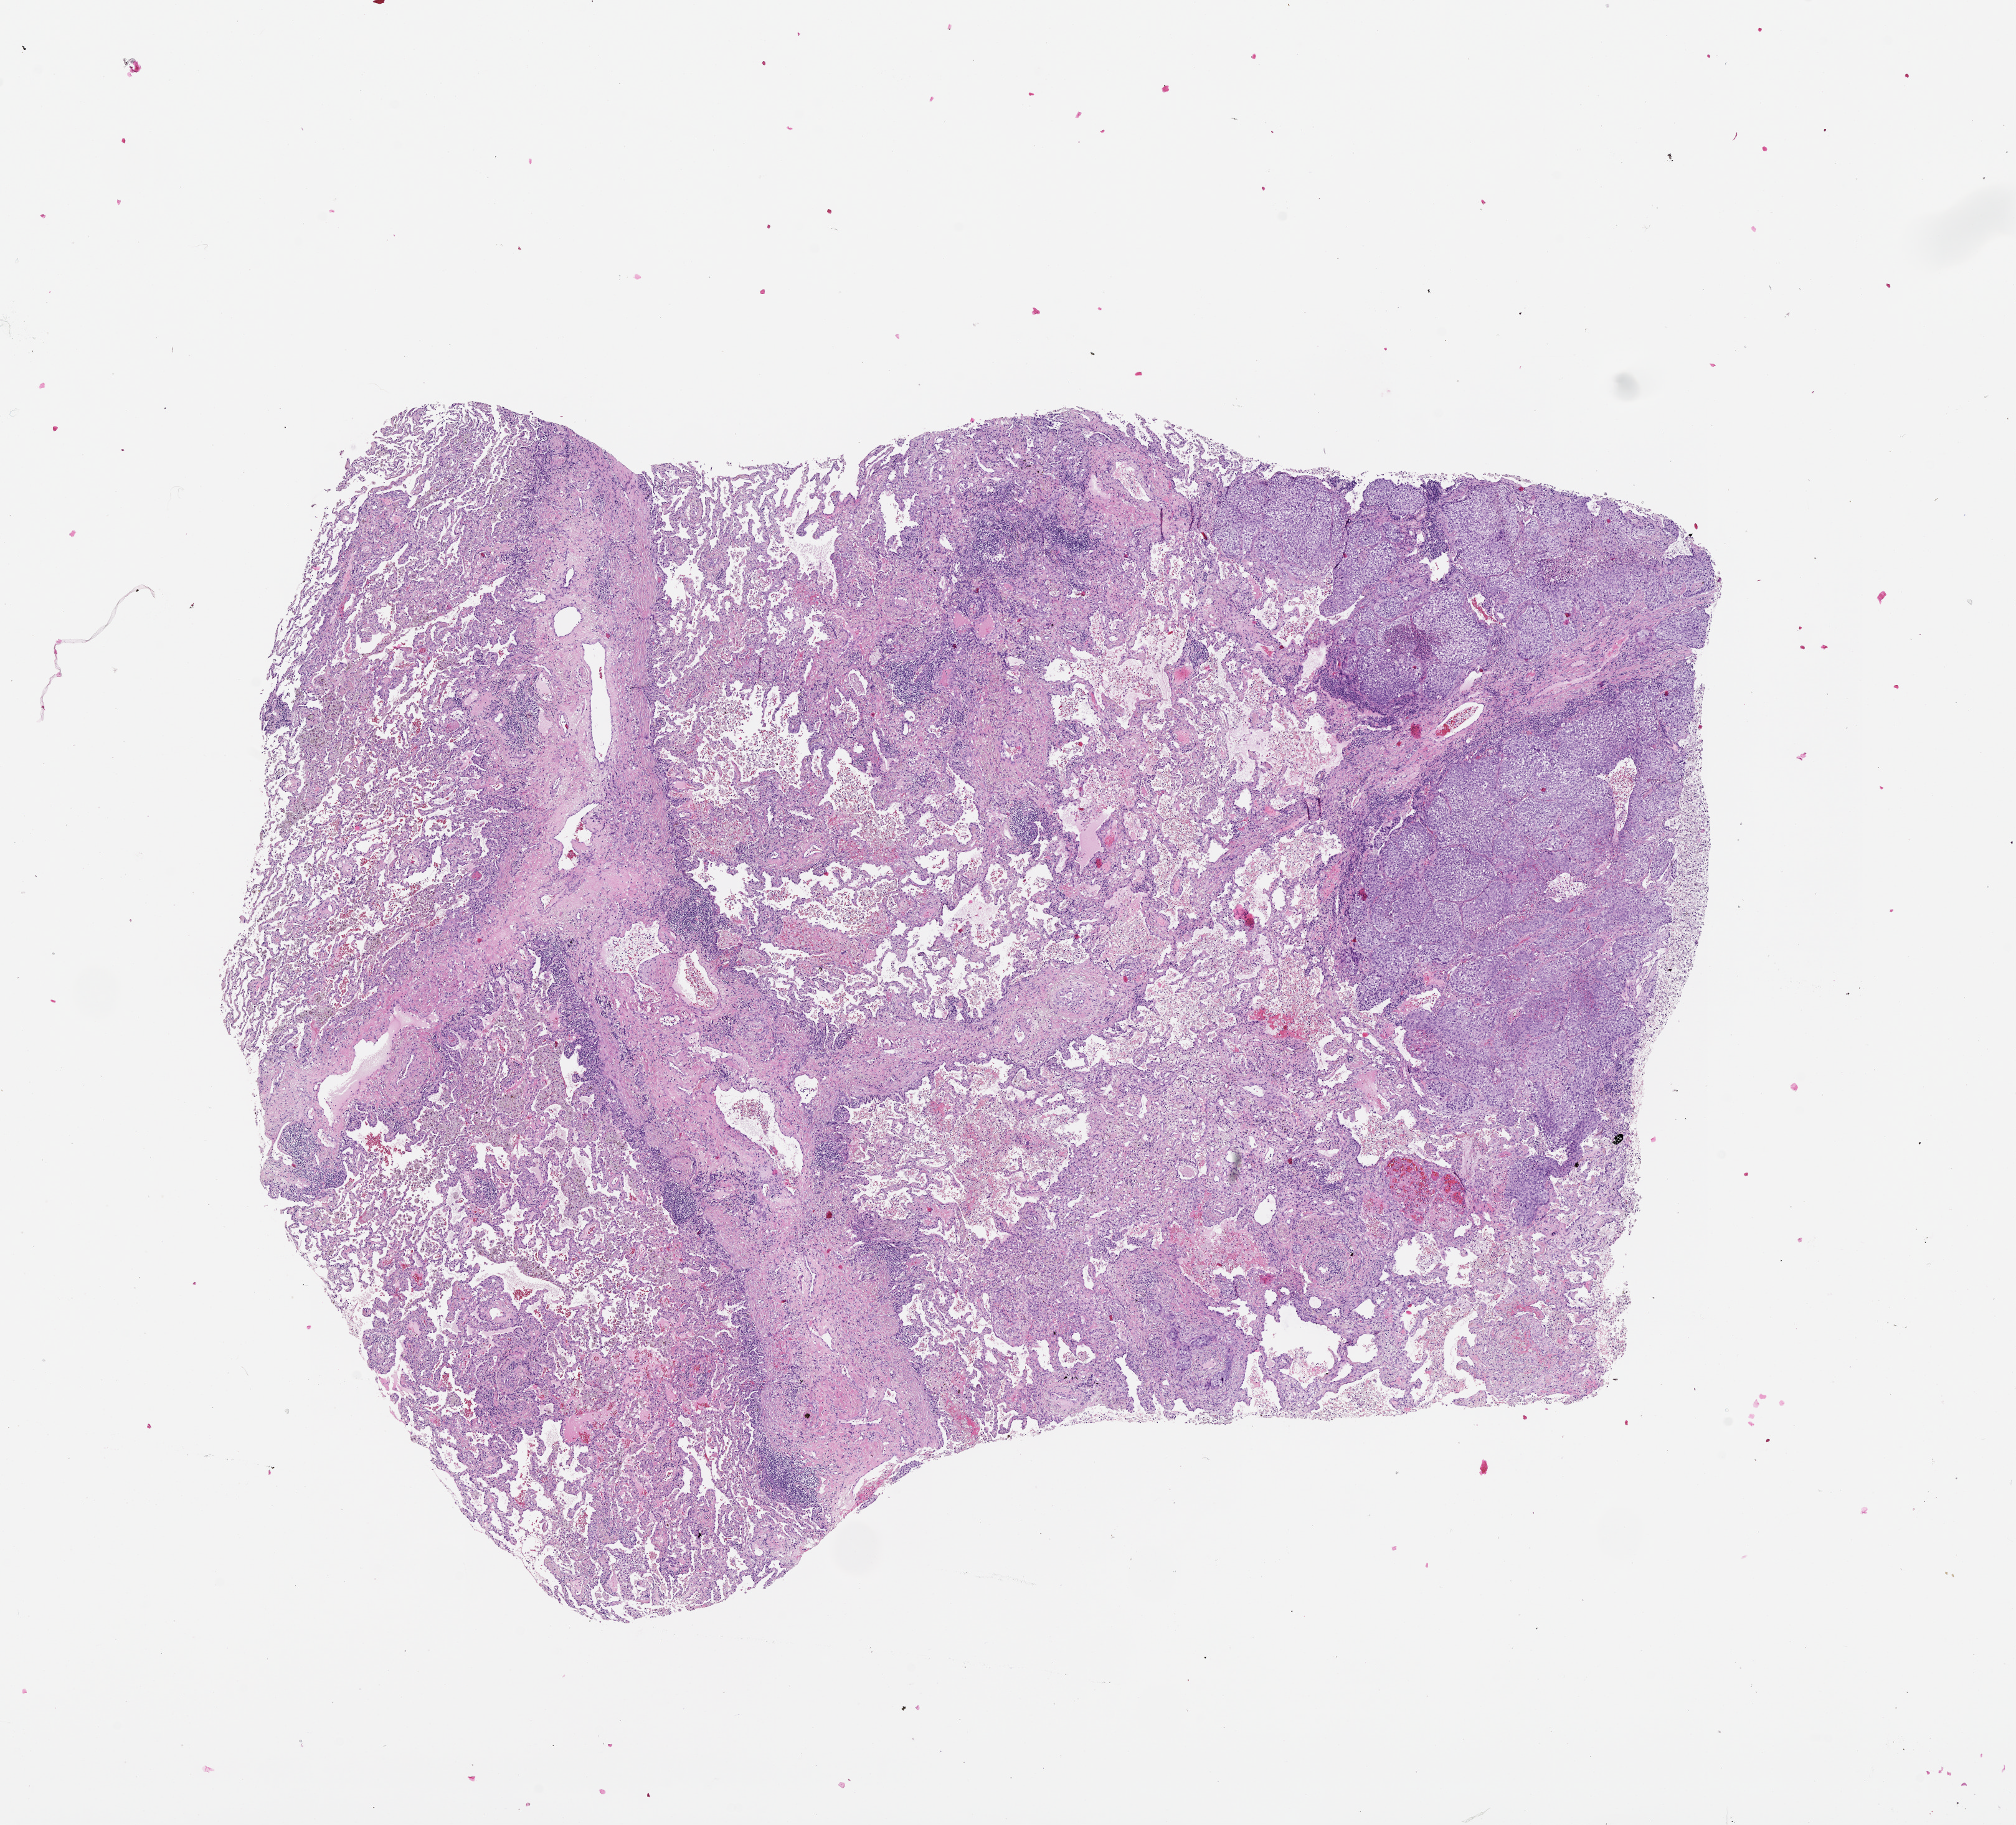
Whole-slide histology image, H&E, whole scanned area (about 13.0 x 11.8 mm, slide scanned at 20x) shown as a low-resolution overview; tumour tissue sample, lung. Patient: male, age 60 years.
- patient diagnosis (cohort enrolment): squamous cell carcinoma (lung)